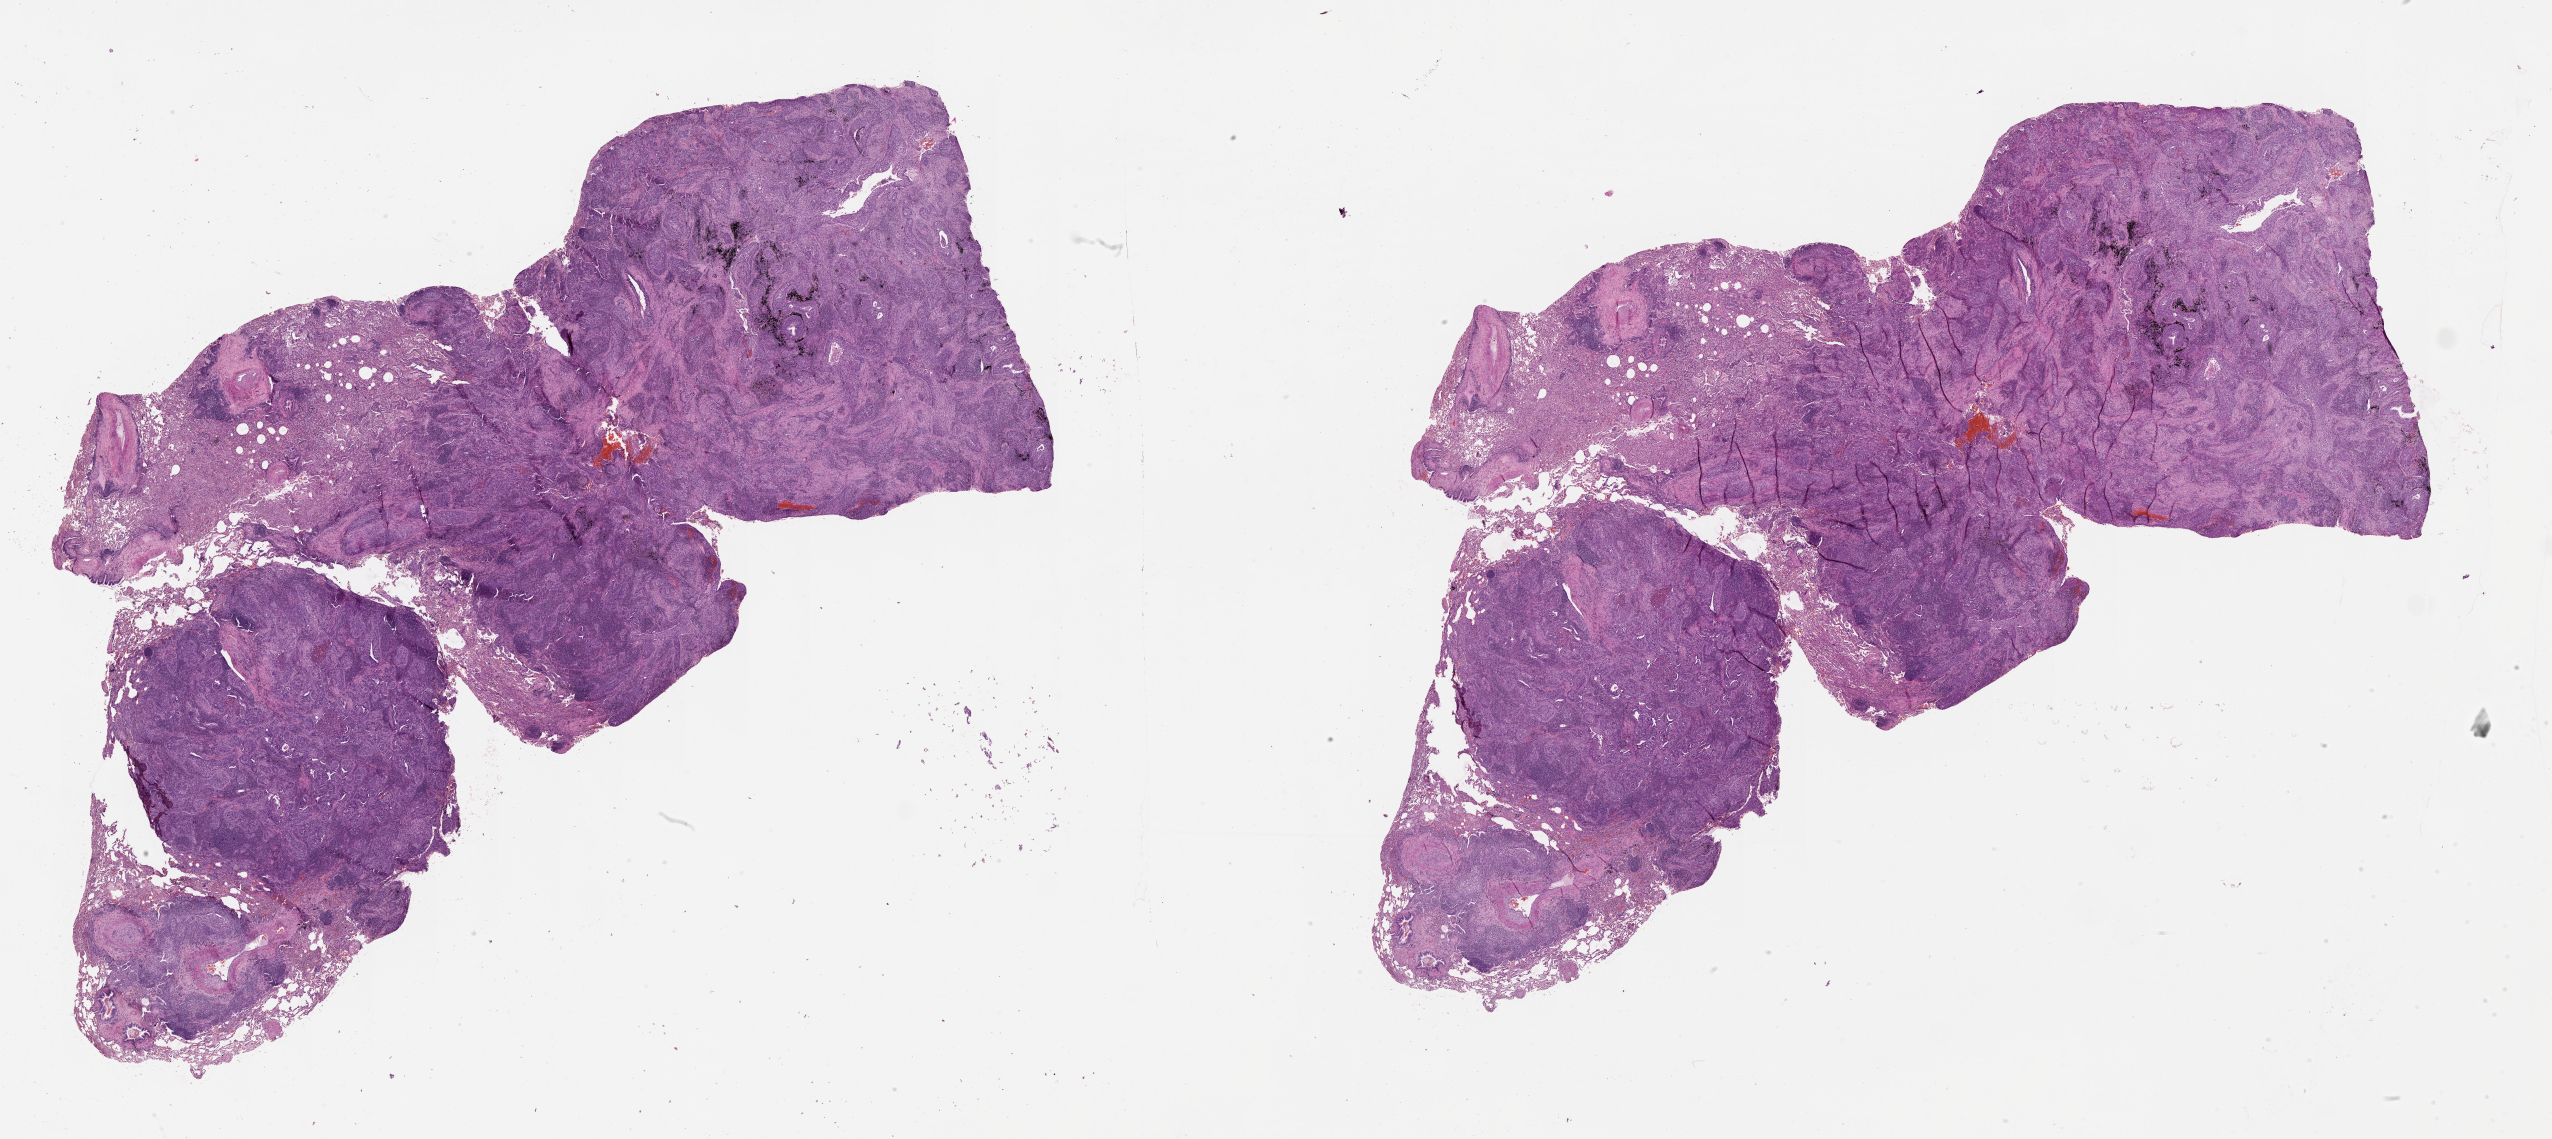
Whole-slide histology image, Hematoxylin and eosin (H&E) stained — low-resolution overview of the scanned area, about 41.1 x 18.3 mm (from a 20x scan); lung, tumour tissue. 74-year-old male patient.
- patient diagnosis (cohort enrolment): squamous cell carcinoma (lung)